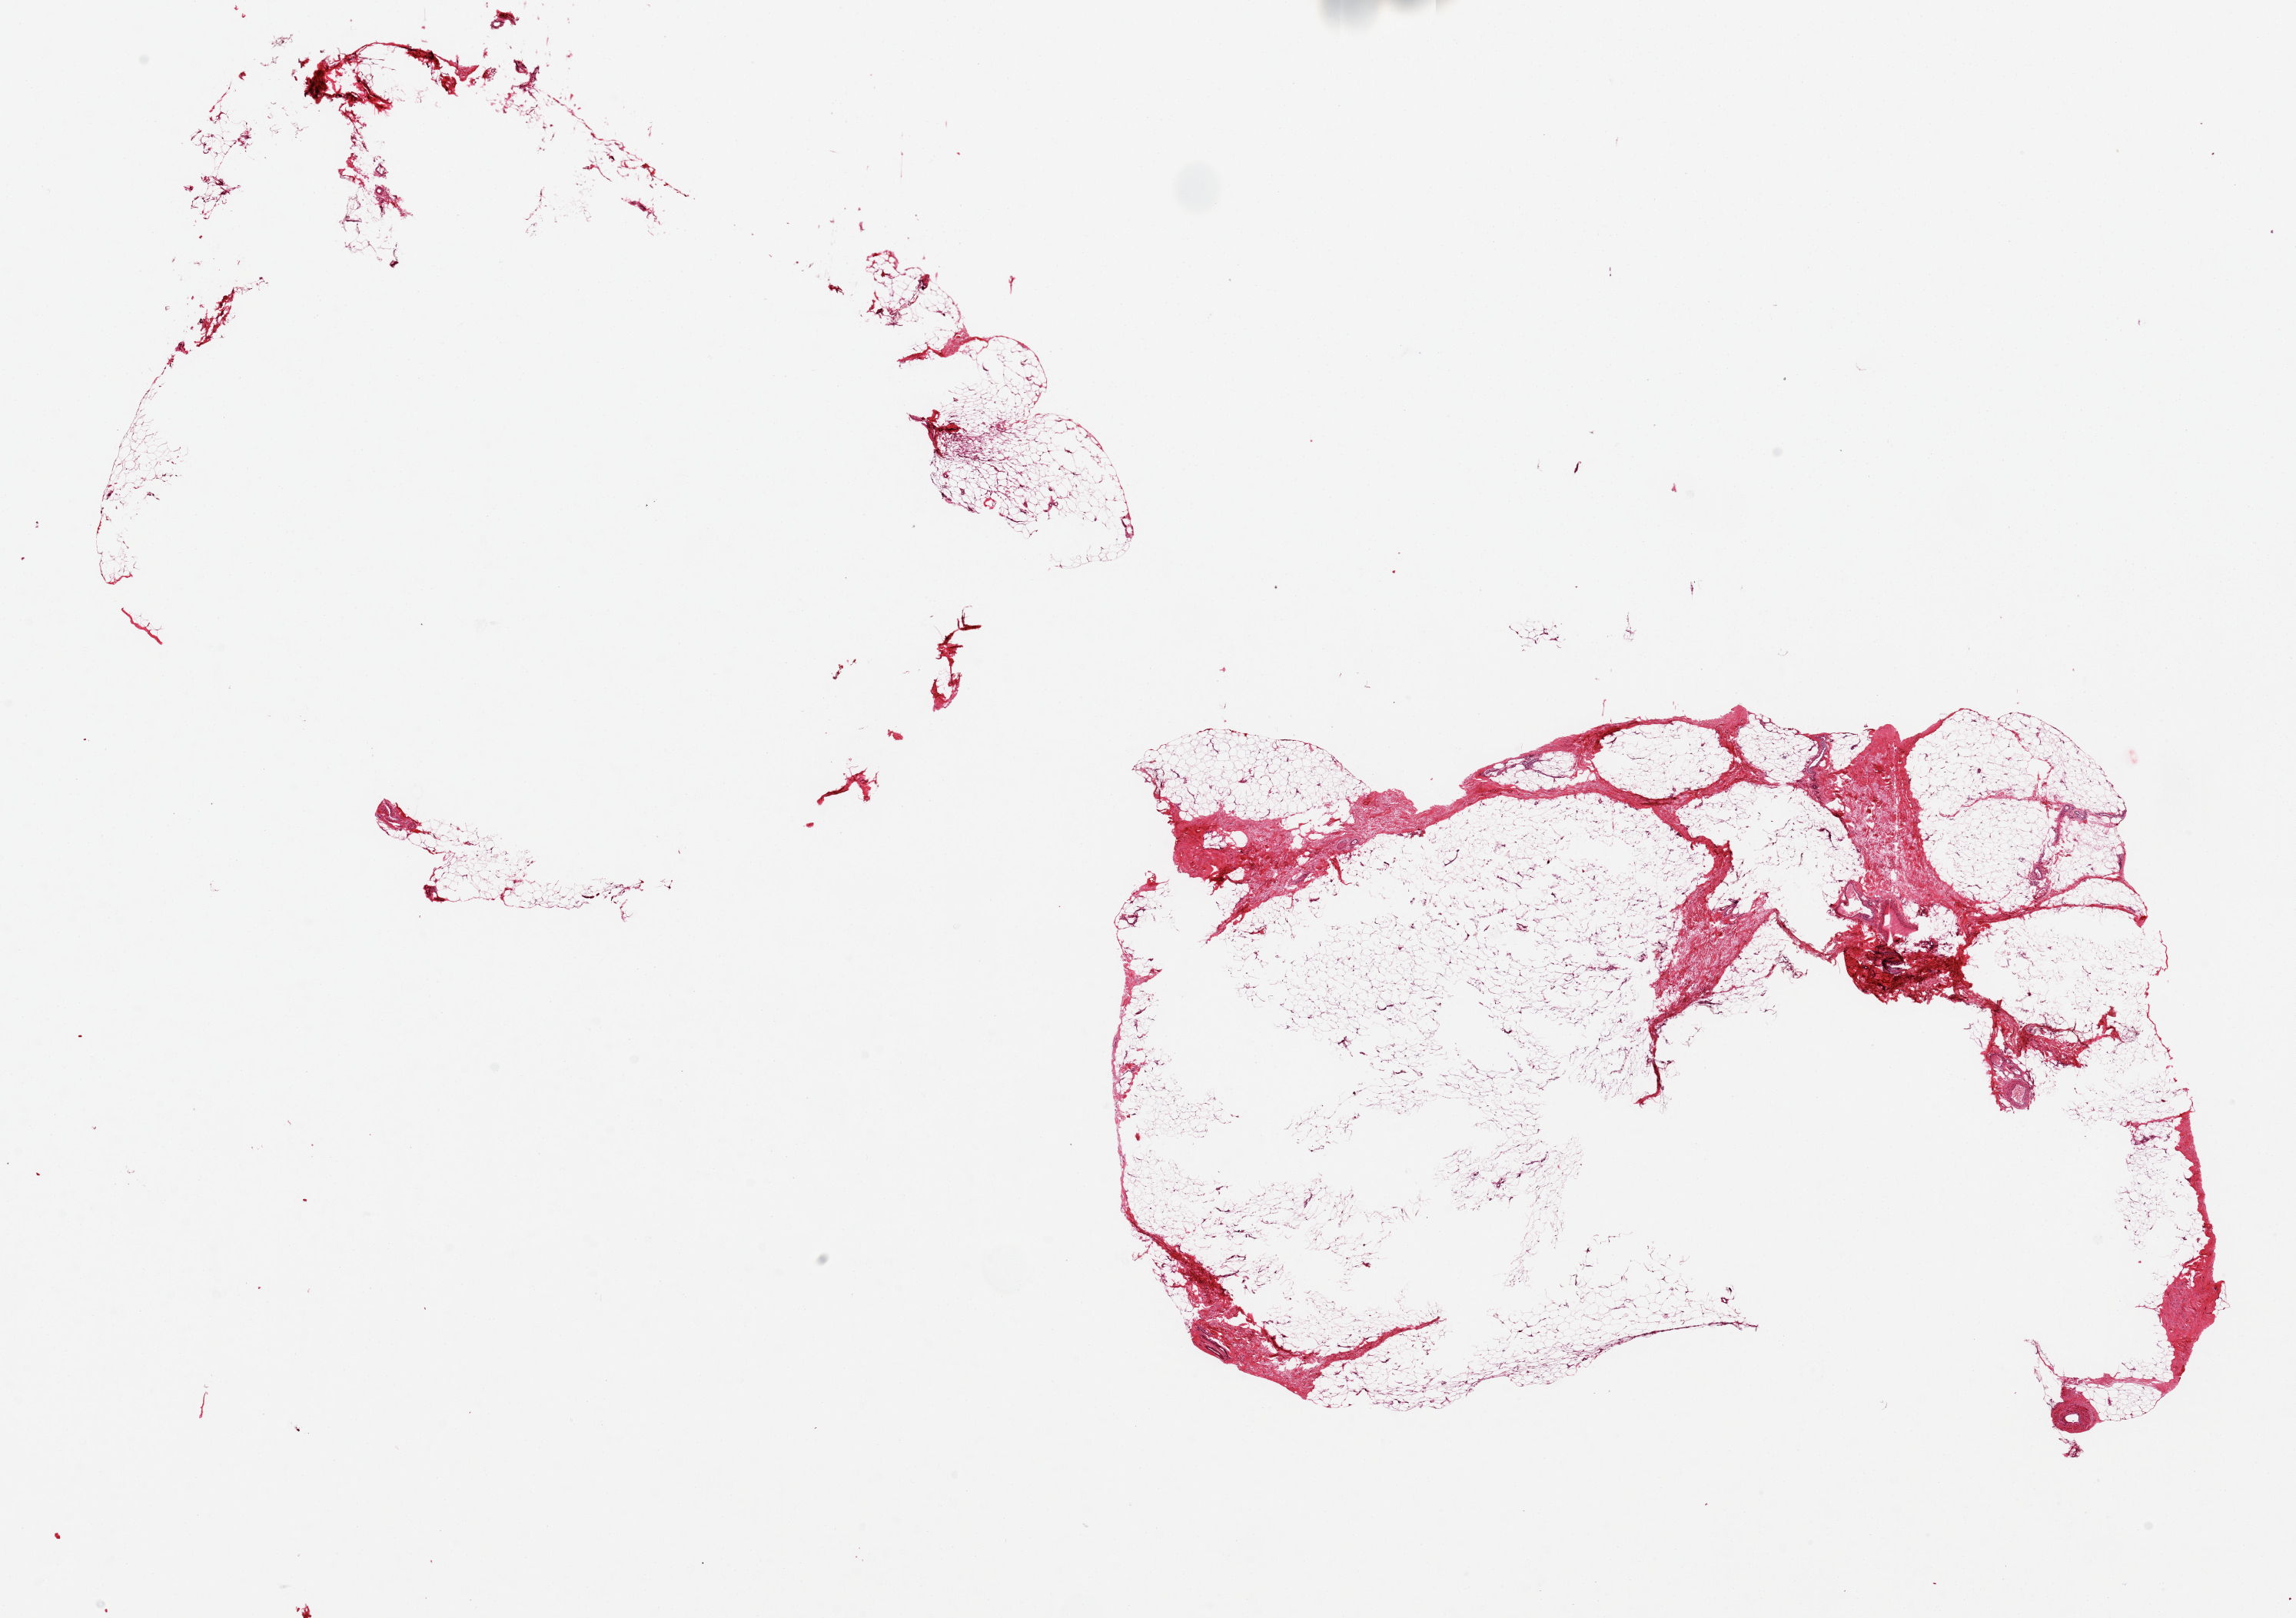
Digitized H&E-stained section — shown as a low-resolution overview of the whole scanned area (about 23.6 x 16.6 mm, from a 20x scan). PAXgene-fixed paraffin-embedded (PFPE) section. Sampled site (target tissue): adipose tissue. Tissue donor sample. Donor: male.
Reviewer comment on this tissue sample: 2 pieces ~10 x 10mm. One with extreme separation but seems well preserved.